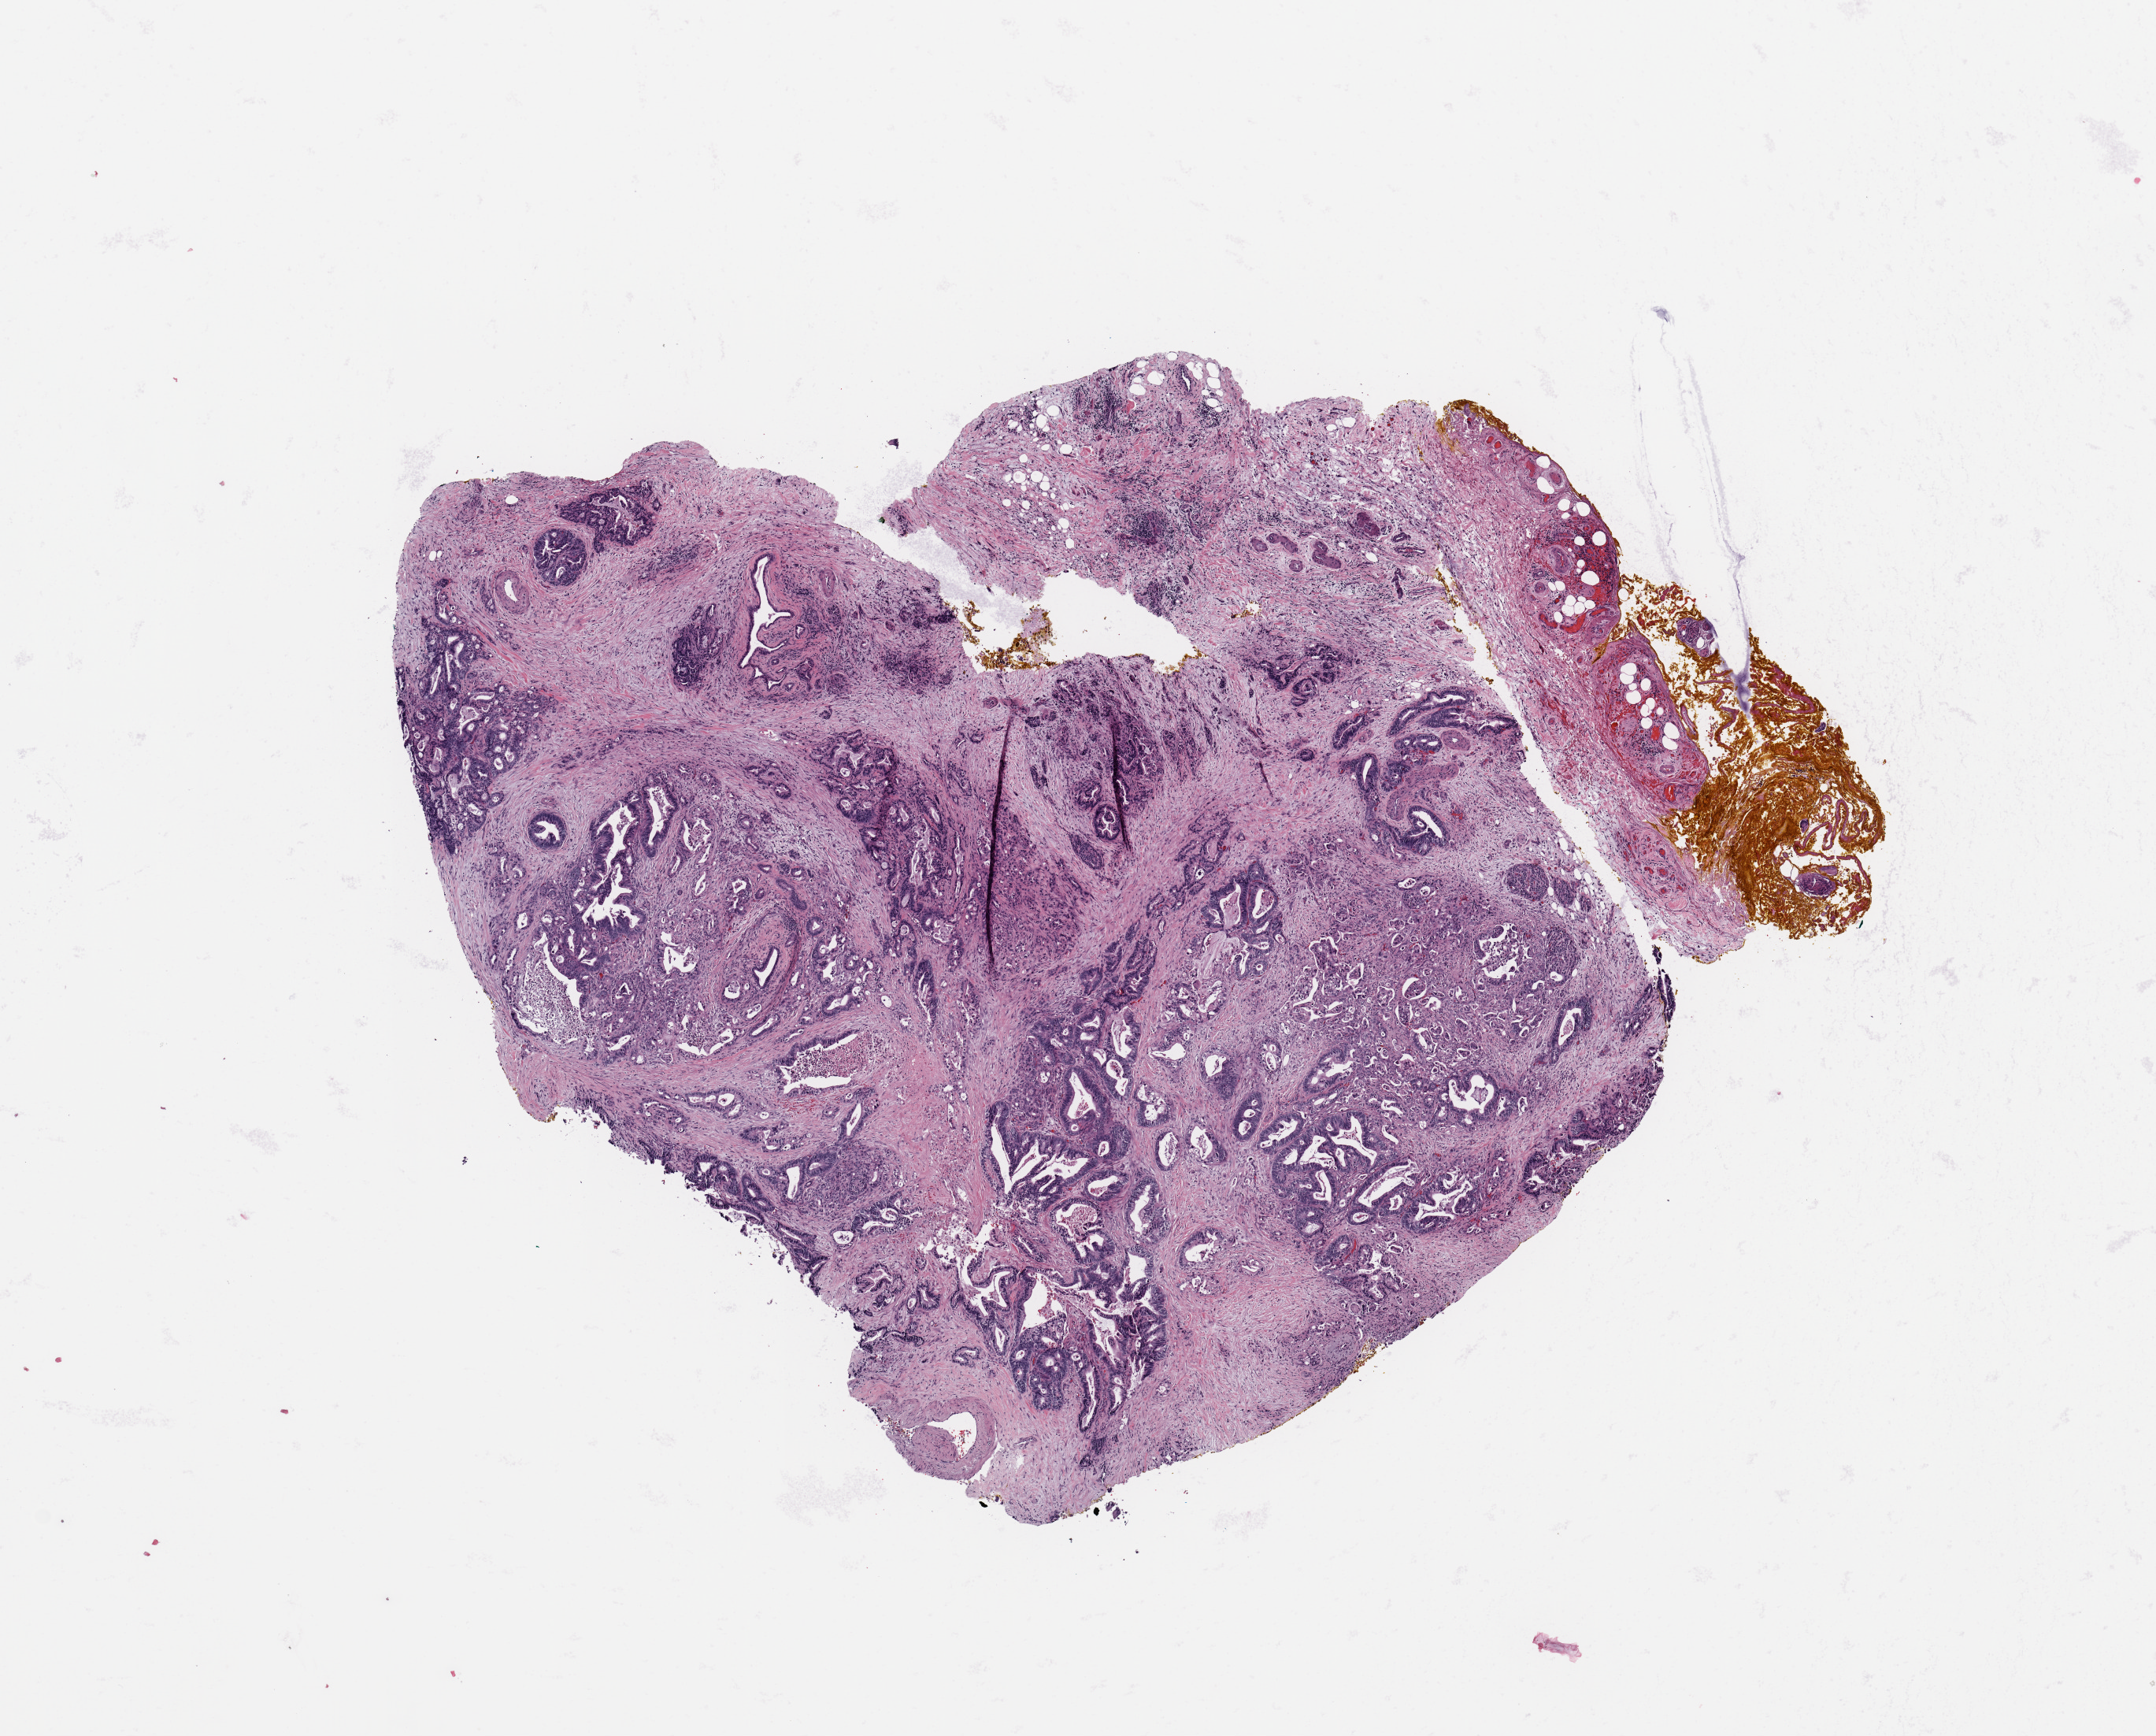
Whole-slide histology image, Hematoxylin and eosin (H&E) stained — low-resolution overview of the scanned area, about 10.8 x 8.7 mm; tumour tissue sample, sampled site: pancreas. Patient: male, age 81 years. Histologic grade: G2 (moderately differentiated). Slide review estimates, as recorded: tumour nuclei 70%, necrosis 0%.
- diagnosis: Infiltrating duct carcinoma, NOS
- primary tumour site (as recorded): head